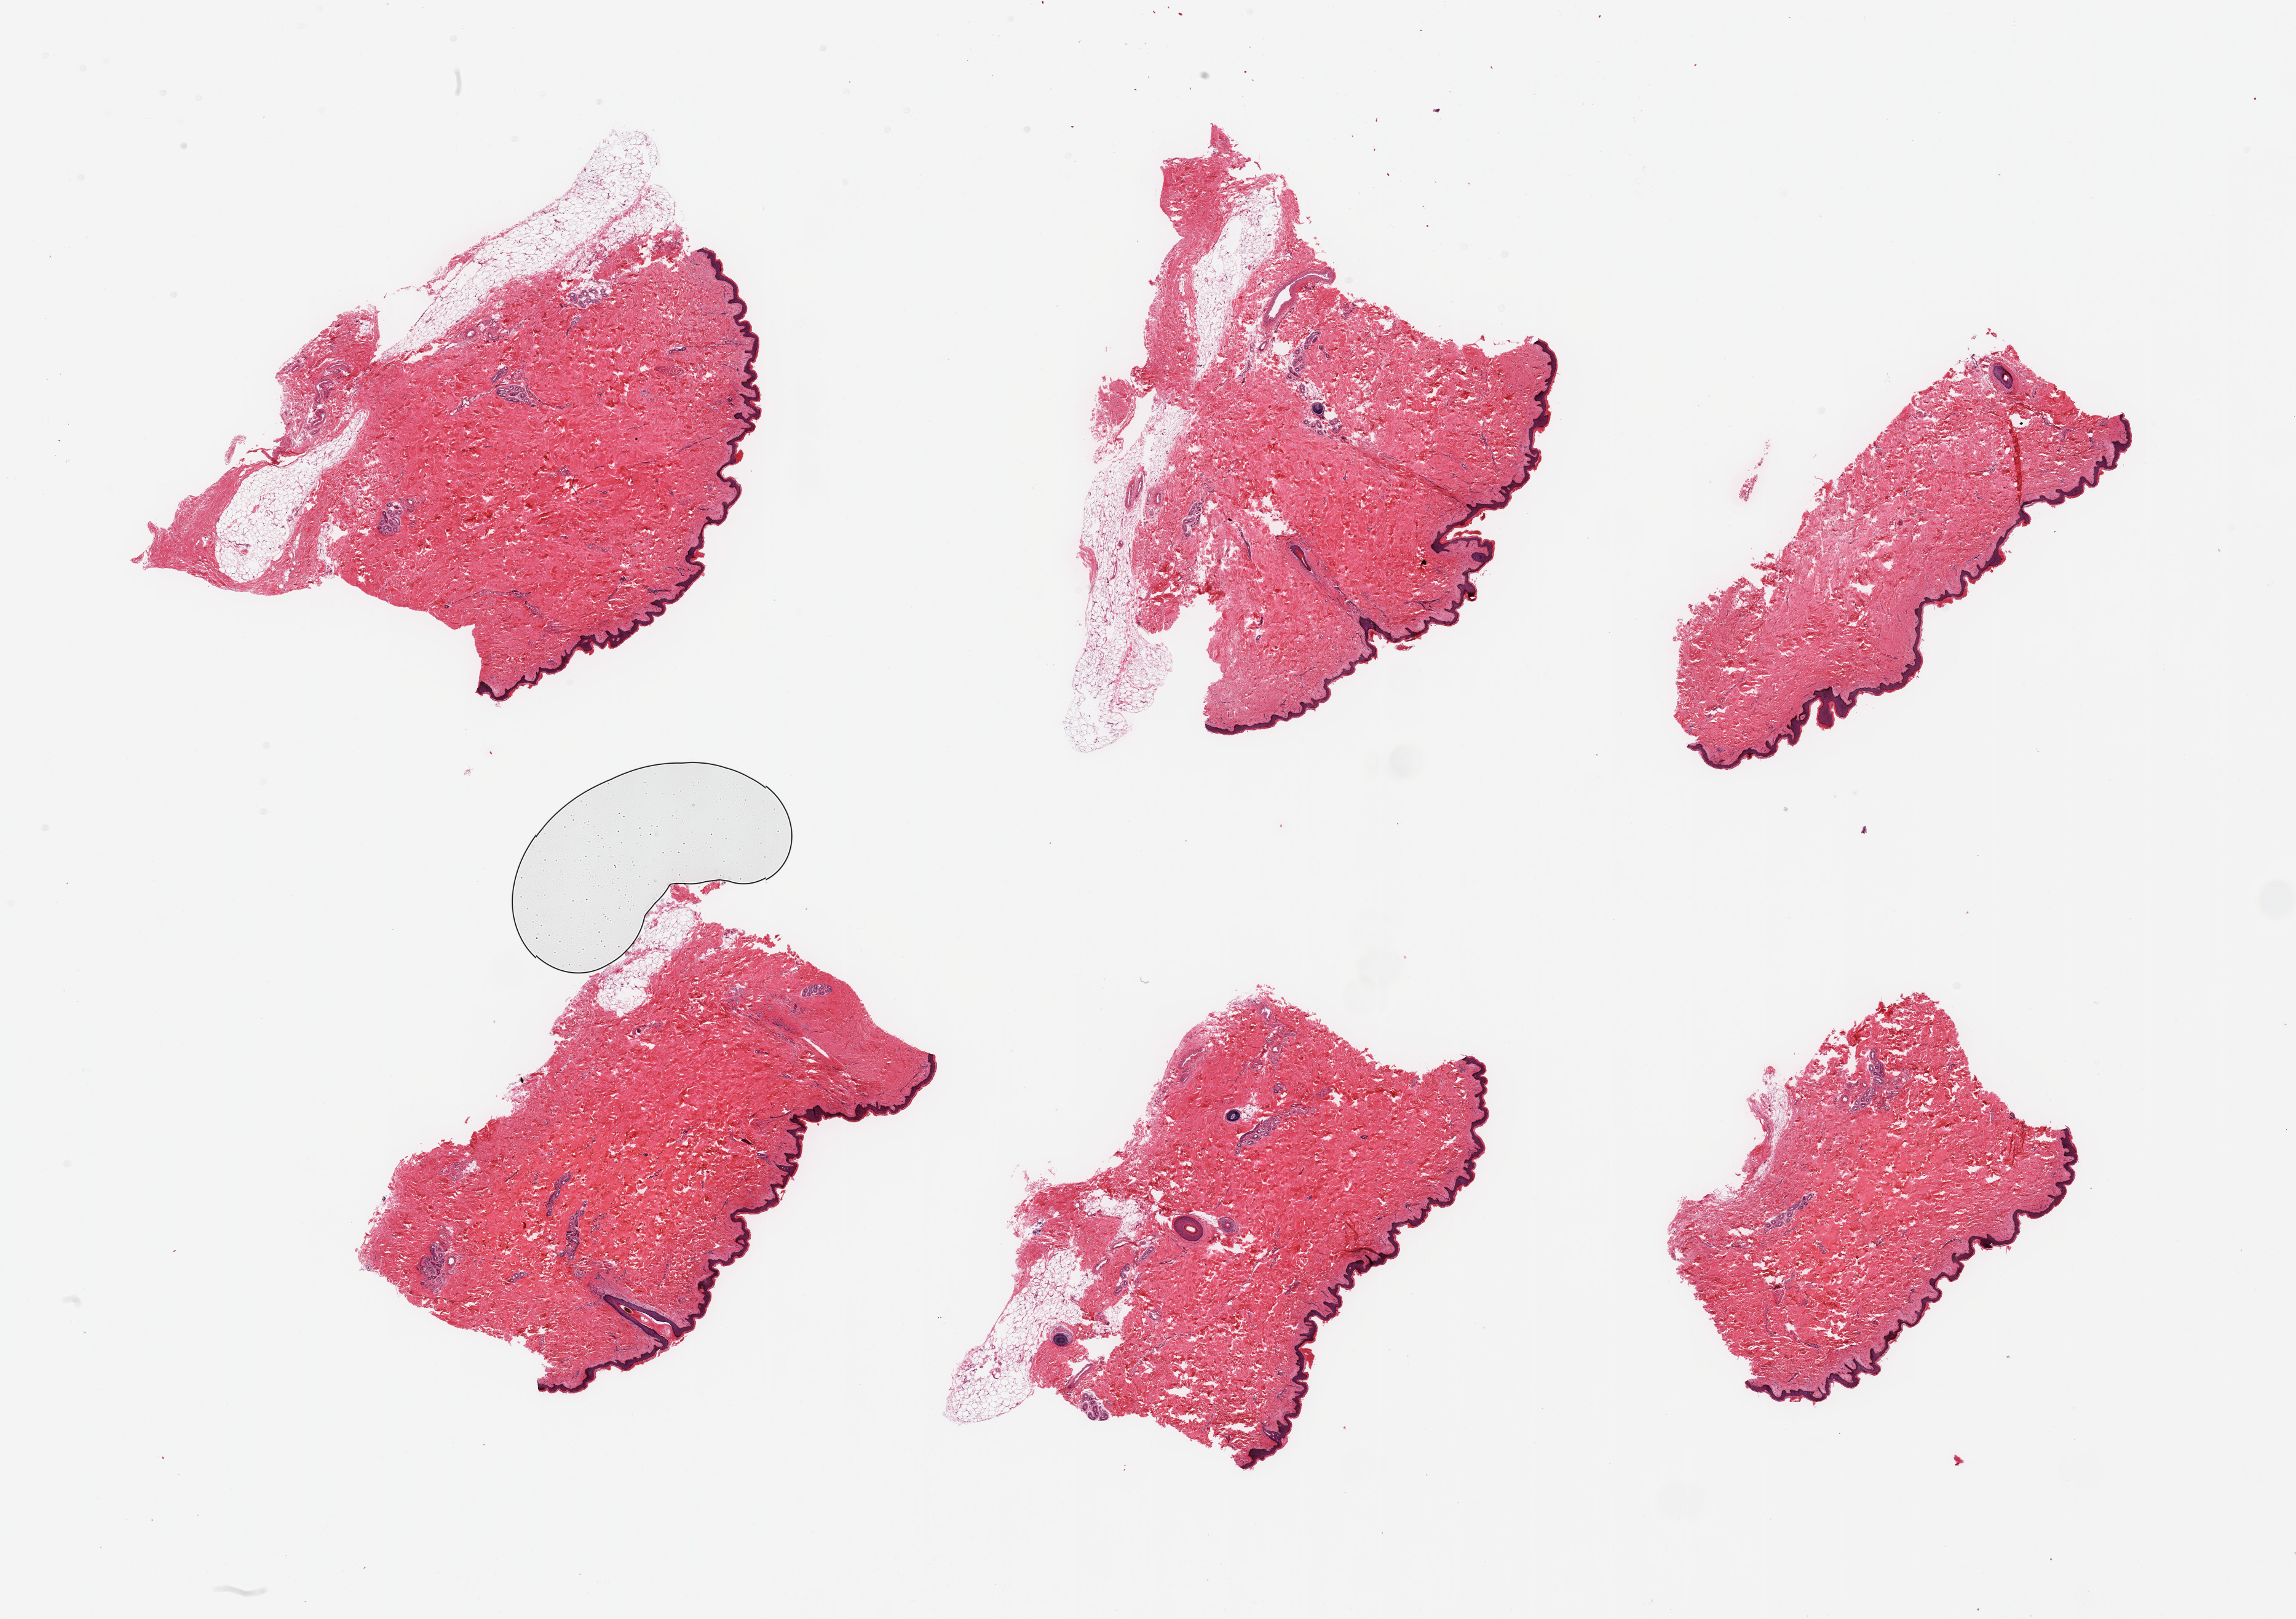
Digitized hematoxylin and eosin (H&E)-stained section — low-resolution overview of the scanned area, about 29.5 x 20.8 mm (from a 20x scan). PAXgene-fixed paraffin-embedded (PFPE) section. Sampled site (target tissue): skin of suprapubic region. Tissue donor sample. Donor: male.
Reviewer comment on this tissue sample: 6 pieces; 4 of 6 pieces contain 5% to 20% subcutaneous/dermal fat.